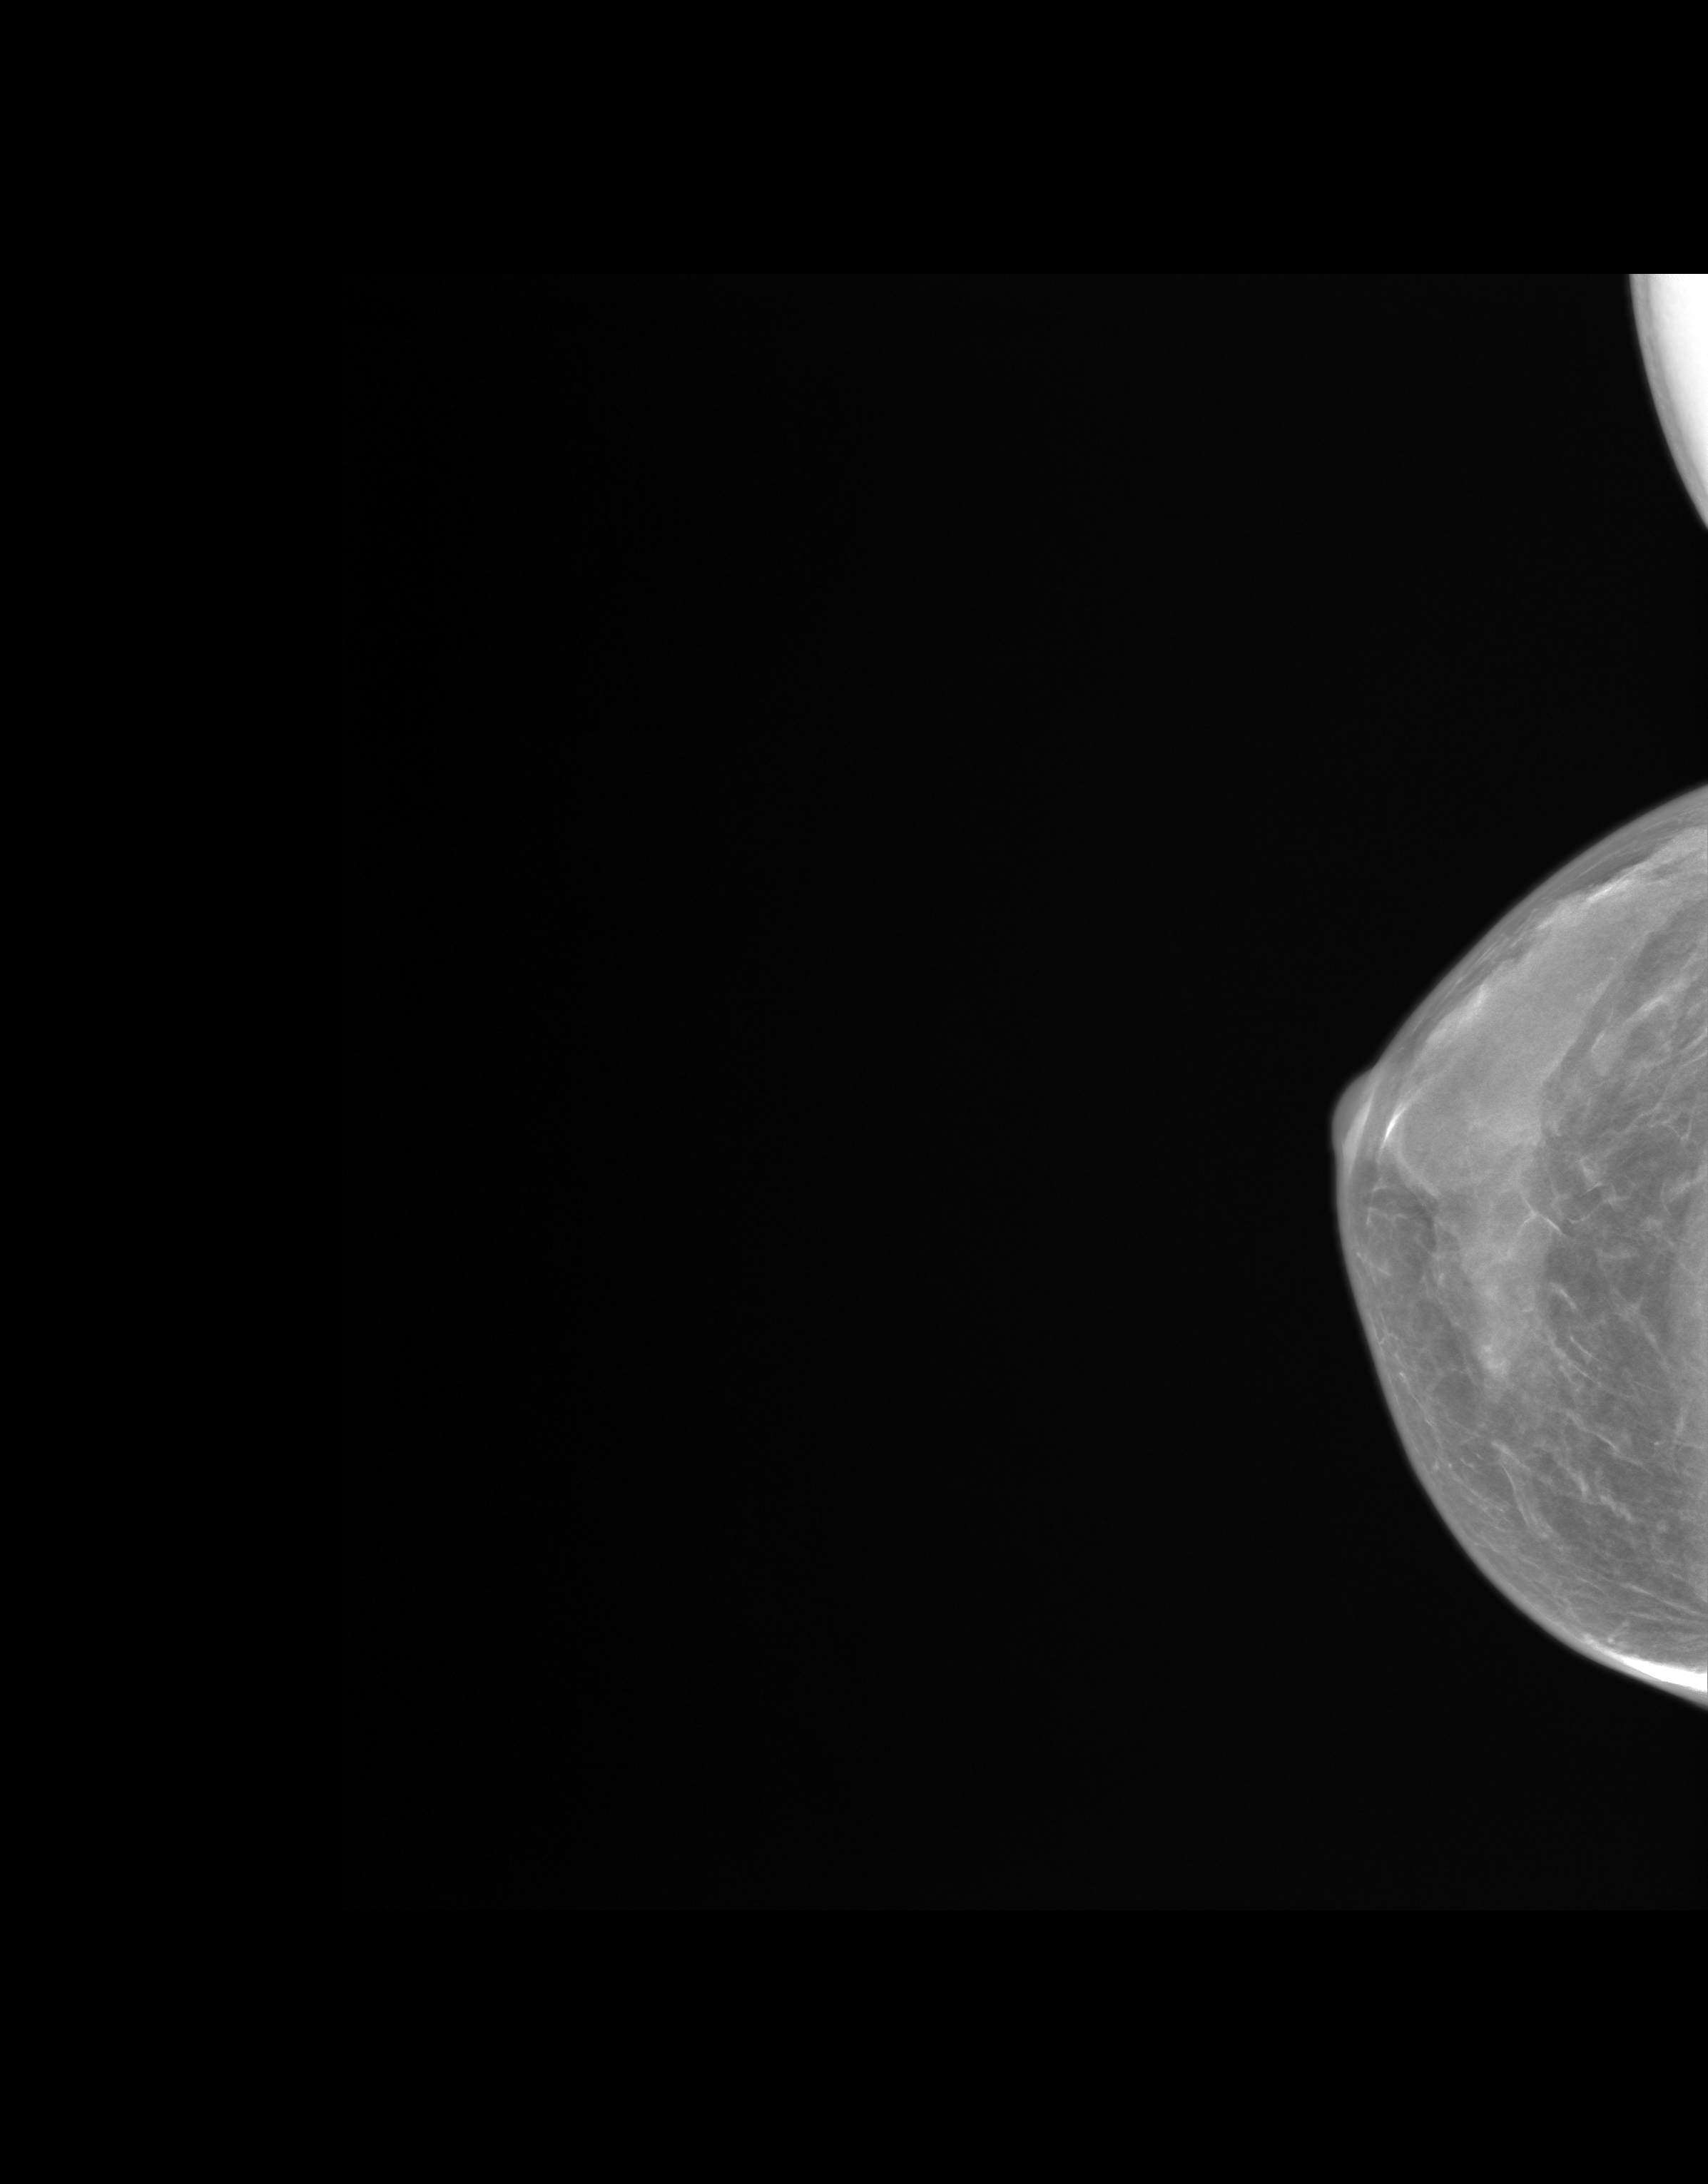
Annual screening mammography examination; system: SenoIris_1SP2(440). Patient: female, 56 years.
Image type: synthesized 2-D view from tomosynthesis. Breast: right. Projection: craniocaudal (CC) view.